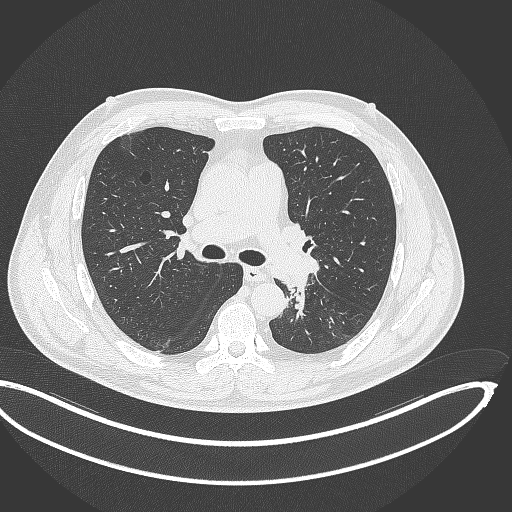
Chest CT, one axial slice; position 218 of 362 along the scan axis; reconstruction kernel B70f; lung window (W 1500 / L -600 HU); 1 mm slice thickness; 512 × 512 image matrix, field of view 442 × 442 mm. Patient: male, 50 years. Case-level facts recorded for this patient, not image findings: clinical TNM (as recorded): T2a N3 M0.
Annotated regions visible in this slice (bounding box drawn by a radiologist):
- lung tumour (recorded histology: squamous cell carcinoma): bounding box [x1, y1, x2, y2] px = [276, 268, 309, 322]